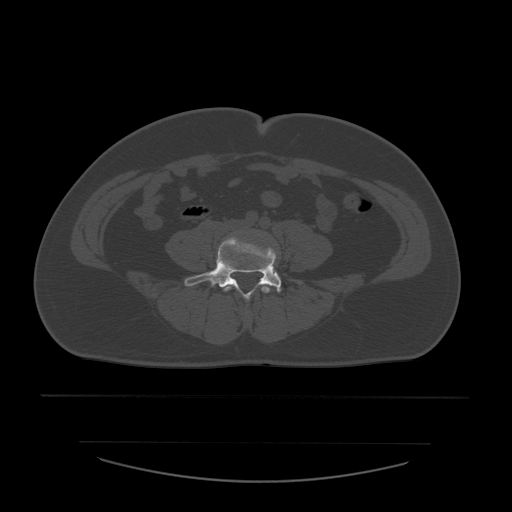
CT including the spine, one axial slice; slice 128 of 532 in the series (ordered by position); reconstruction kernel STANDARD; 120 kVp; bone window (W 1800 / L 400 HU); 1.25 mm slice thickness; 512 × 512 image matrix, field of view 441 × 441 mm. Patient age 44 years. From the clinical record (not read from this slice): primary cancer: soft tissue sarcoma.
Outlined on this slice (semi-automatic segmentation, software-assisted and operator-edited):
- L4 vertebra: box from (x=223, y=286) to (x=271, y=294) px
- L5 vertebra: (x=184, y=238)–(x=302, y=299)